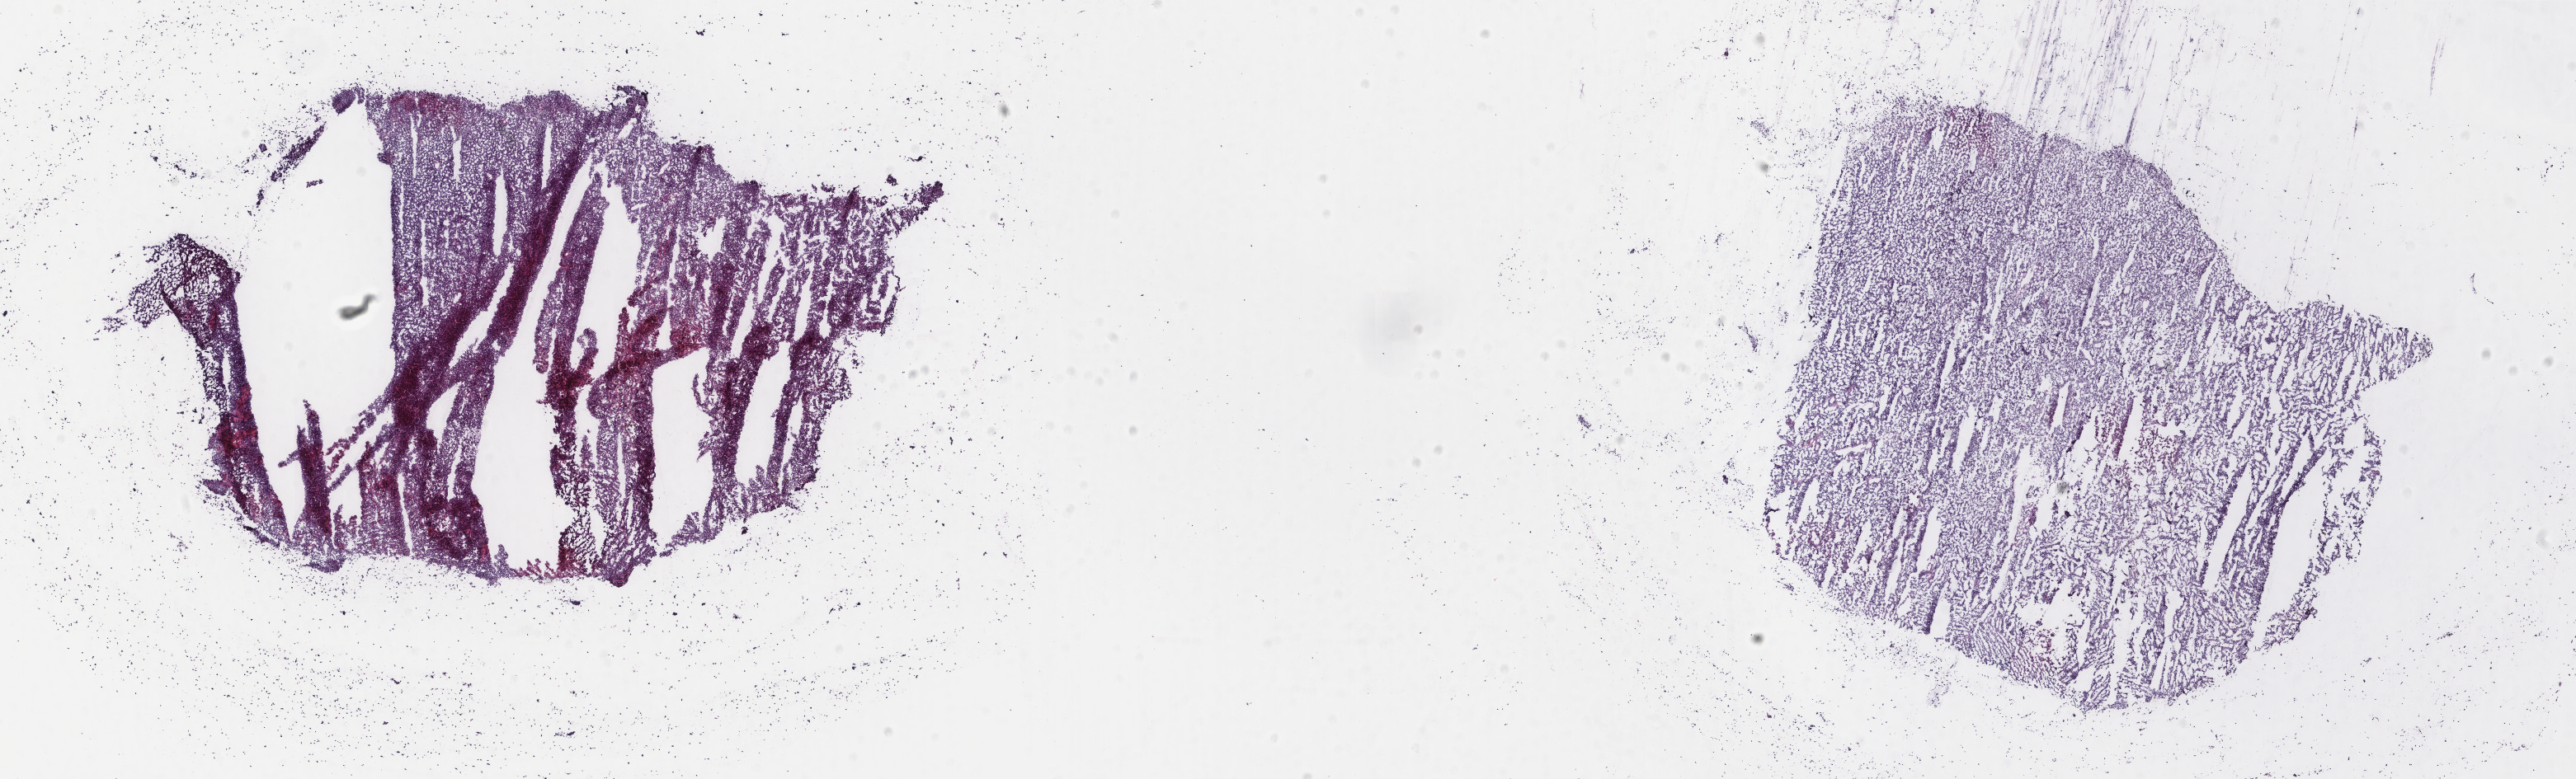
H&E whole-slide image, low-resolution overview of the scanned area, about 24.8 x 7.5 mm, frozen section, metastatic tumour sample, sampled site not recorded. Patient: male, age at initial diagnosis 57 years. Composition of this section per pathologist review: tumour cells 95%, tumour nuclei 95%, normal cells 0%, stromal cells 4%, necrosis 1%. Inflammatory infiltration, as recorded: lymphocyte infiltration 1%, monocyte infiltration 0%, neutrophil infiltration 0%.
- this section: metastatic tumour tissue
- patient diagnosis: Malignant melanoma, NOS